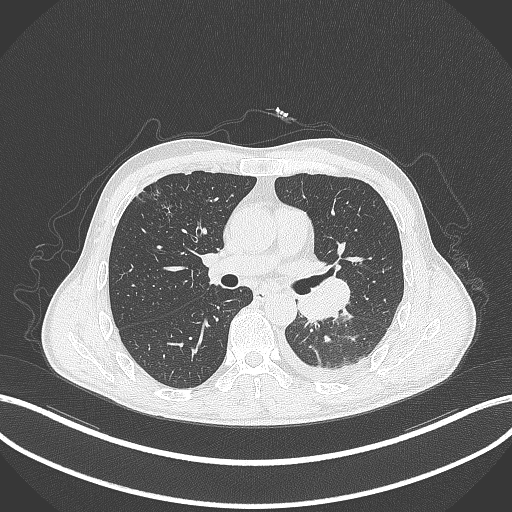
Chest CT, one axial slice; position 182 of 295 along the scan axis; reconstruction kernel B70f; lung window (W 1500 / L -600 HU); 1 mm slice thickness; 512 × 512 image matrix, field of view 400 × 400 mm. Patient: male, 47 years. Case-level facts recorded for this patient, not image findings: clinical TNM (as recorded): T3 N1 M1c.
Structures marked on this image (rectangle marked by the reading radiologist):
- lung tumour (recorded histology: small cell carcinoma): box from (x=295, y=276) to (x=352, y=325) px